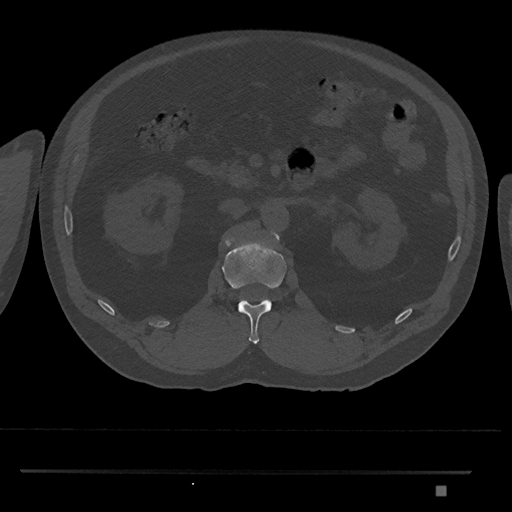
CT including the spine, one axial slice; position 808 of 1134 along the scan axis; reconstruction kernel Br40s/3; 120 kVp; bone window (W 1800 / L 400 HU); 0.5 mm slice thickness; 512 × 512 image matrix, field of view 429 × 429 mm. Male patient, age 65 years. Case-level facts recorded for this patient, not image findings: primary cancer: prostate.
Annotated regions visible in this slice (semi-automatically segmented with operator editing):
- L1 vertebra: bounding box <222,231,287,344> (left, top, right, bottom; pixels)